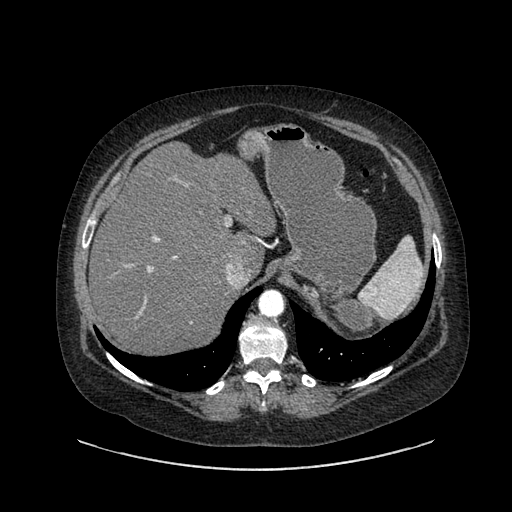
Contrast-enhanced abdominal CT, one axial slice. Position 639 of 769 along the scan axis. 120 kVp. Soft-tissue window (W 400 / L 40 HU). 512 × 512 image matrix. Female patient, age 61 years. From the clinical record (not read from this slice): diagnosis: adrenocortical carcinoma; tumour side: left adrenal; tumour size at pathology: 13 cm; Ki-67 index: 79 %; stage (as recorded): 2.
Structures marked on this image (semi-automatically segmented with operator editing):
- mass: bounding box [x1, y1, x2, y2] px = [325, 293, 374, 335]